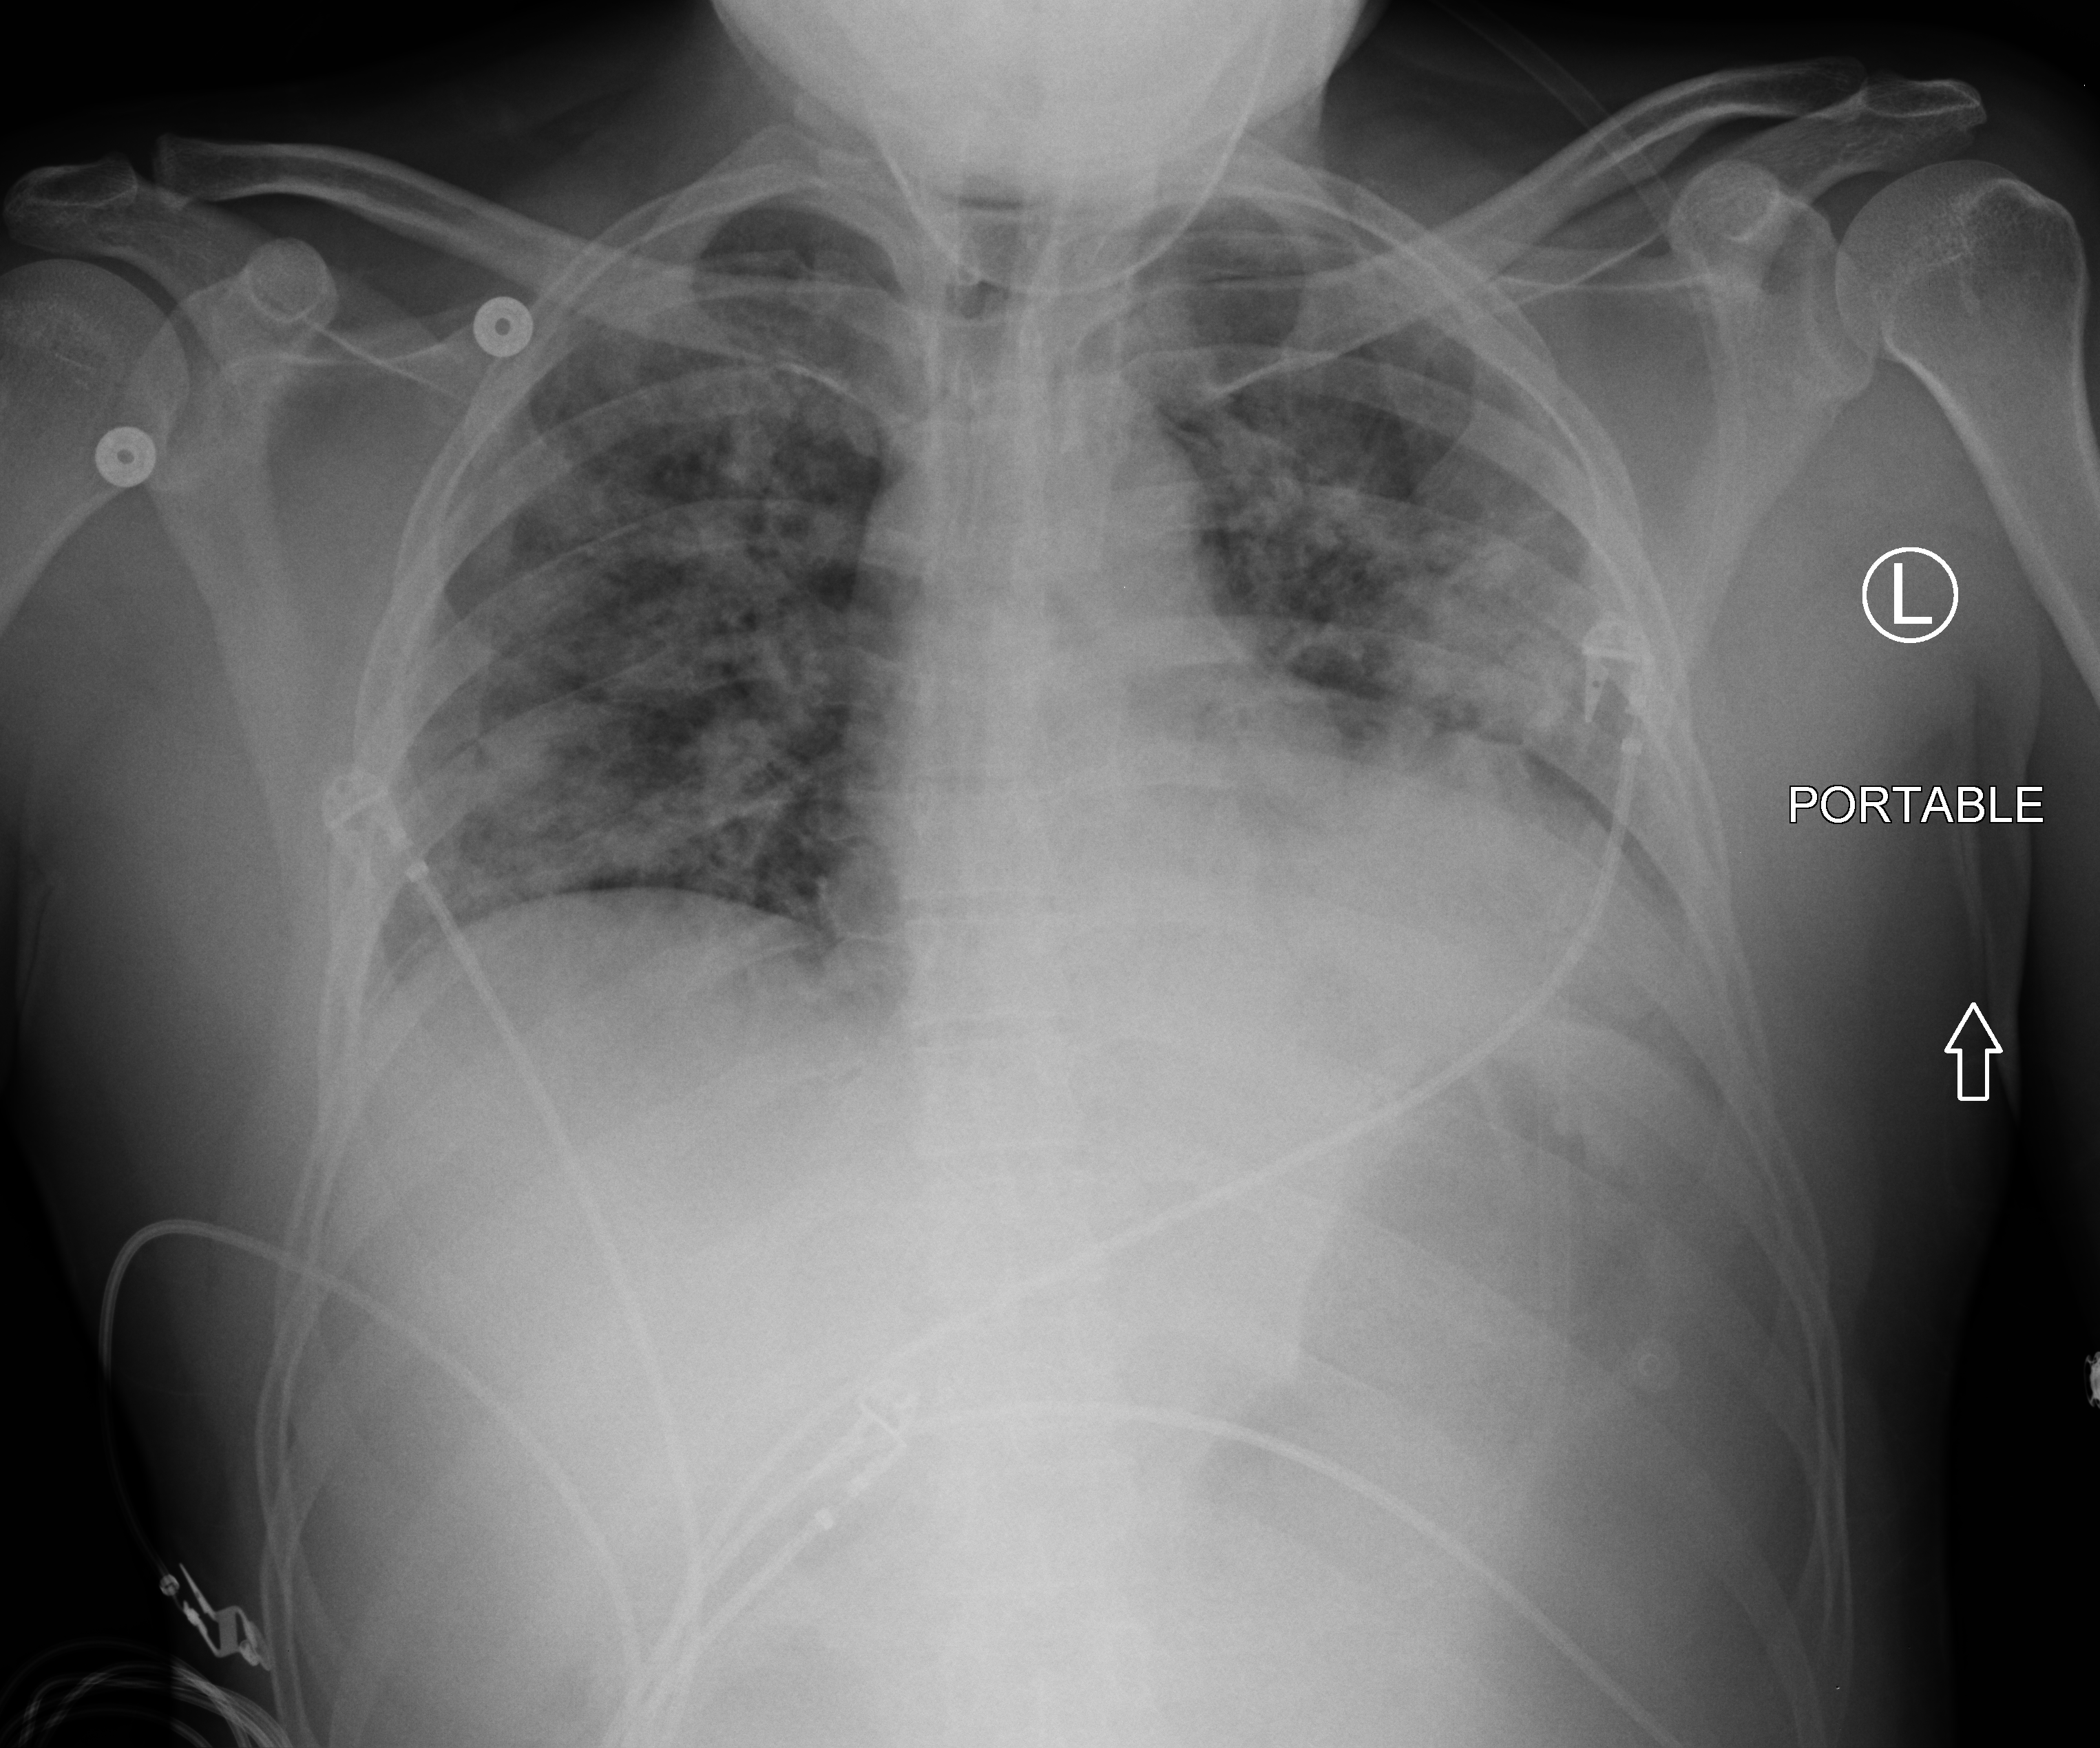
Portable chest radiograph, anteroposterior (AP) projection. Patient hospitalised with COVID-19; male, aged 18–59 years.
Admission-level facts for this patient (not findings on this image; timing relative to this image not recorded):
- admitted to intensive care during this hospital stay: yes
- other chronic lung disease (admission record): no
- mechanically ventilated during this hospital stay: yes